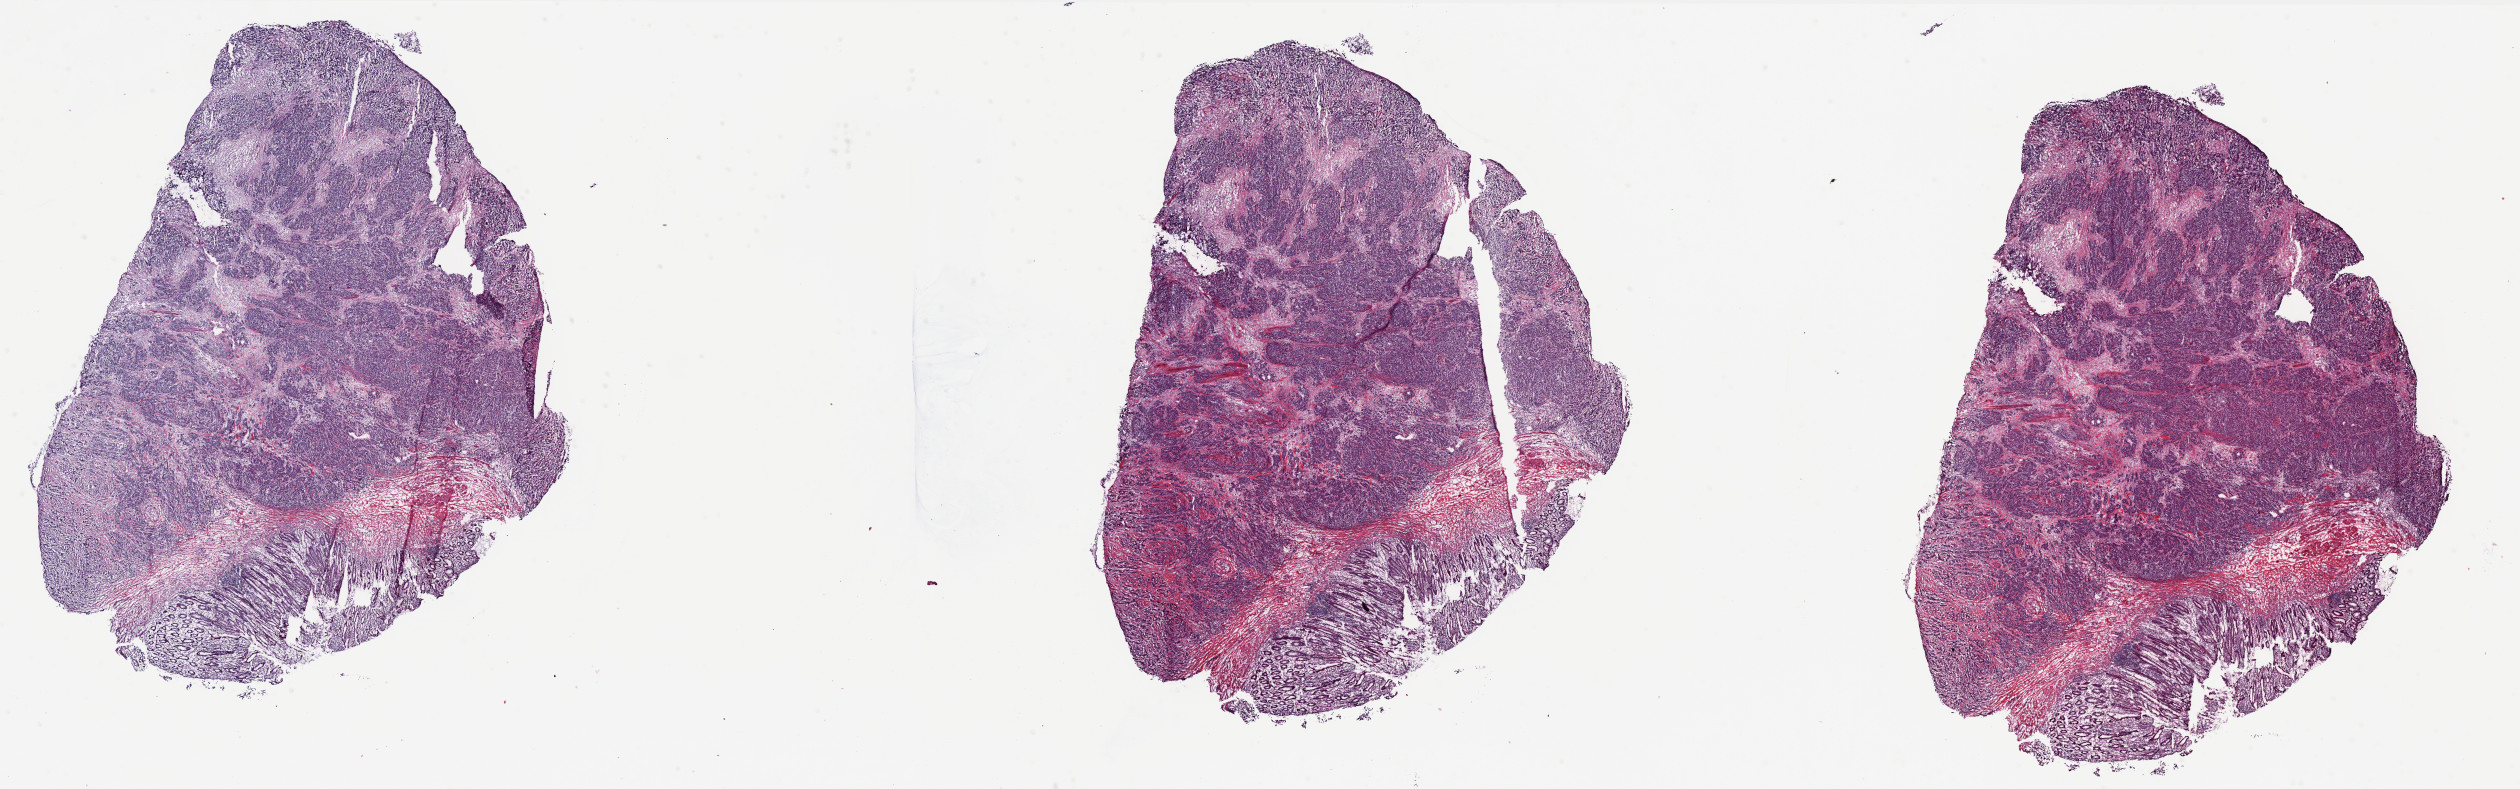
Whole-slide histology image, H&E — whole scanned area (about 40.4 x 12.7 mm) shown as a low-resolution overview. Frozen section from the bottom of the tissue portion. Primary tumour sample from the colon. Patient: female, age at initial diagnosis 84 years. Pathologist review of this section (percent, as recorded): tumour cells 69%, tumour nuclei 80%, normal cells 25%, stromal cells 5%, necrosis 1%. Inflammatory infiltration, as recorded: lymphocyte infiltration 5%, monocyte infiltration 0%, neutrophil infiltration 1%.
- pathologic diagnosis: Adenocarcinoma, NOS (cecum)
- lymph nodes positive (case pathology): 0 of 18 examined
- AJCC pathologic stage: IIA (6th edition)